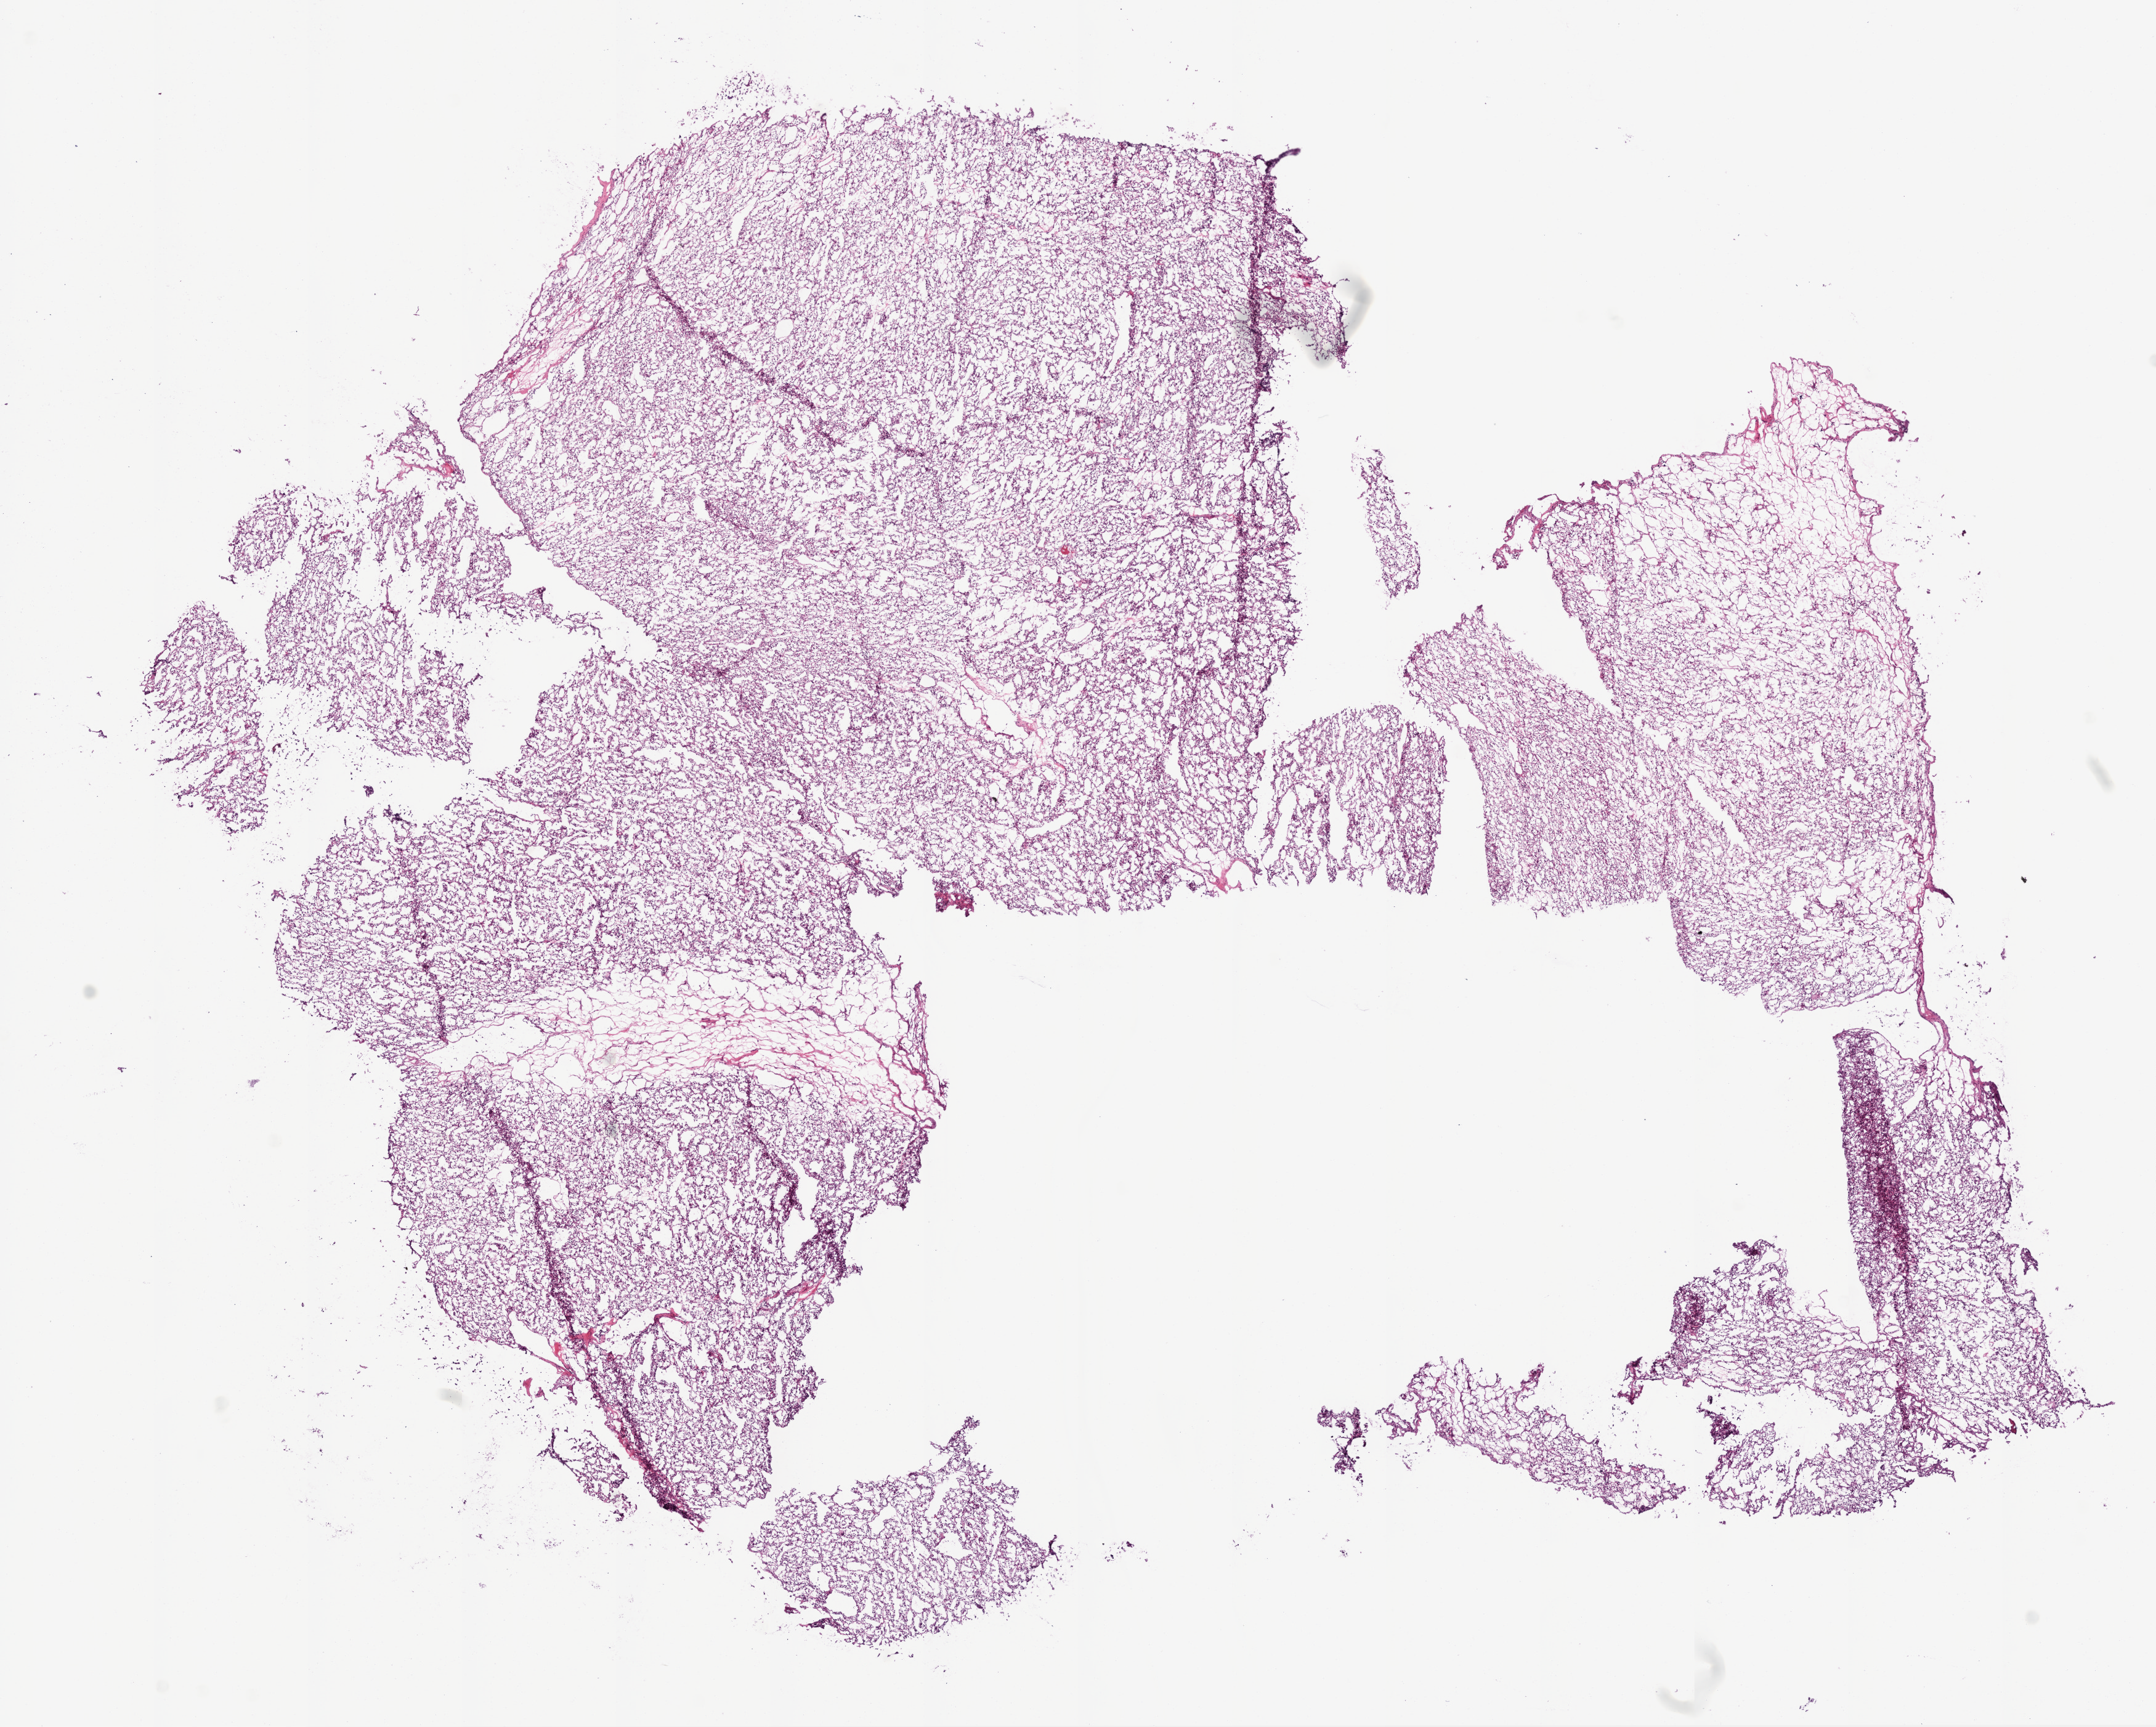
H&E-stained whole-slide image, a low-resolution overview of the entire scanned area, about 14.0 x 11.2 mm (acquisition: 20x scan); frozen section; sample: primary tumour, kidney. Patient: female, age at initial diagnosis 64 years. Histologic grade: G1 (well differentiated). Composition of this section per pathologist review: tumour cells 90%, tumour nuclei 90%, normal cells 0%, stromal cells 10%, necrosis 0%.
TNM: T1b N0 M0. Lymph nodes positive (case pathology): 0 of 2 examined. Histologic diagnosis: Clear cell adenocarcinoma, NOS. AJCC pathologic stage: I. Laterality: right.